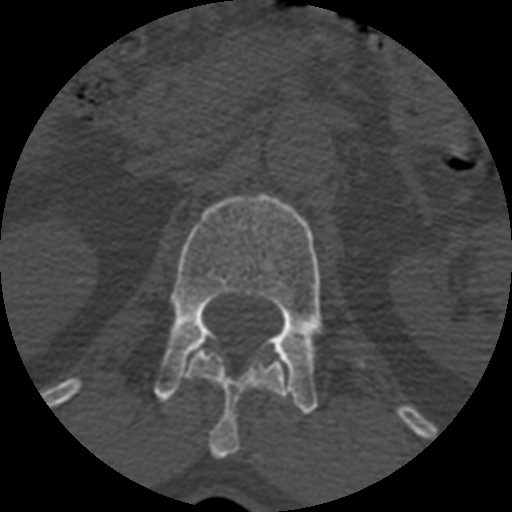
CT including the spine, one axial slice; position 368 of 399 along the scan axis; 120 kVp; bone window (W 1800 / L 400 HU); 1.25 mm slice thickness; 512 × 512 image matrix. Patient age 71 years. Case-level facts recorded for this patient, not image findings: primary cancer: prostate.
Structures marked on this image (semi-automatic segmentation, software-assisted and operator-edited):
- L1 vertebra: bounding box (x1, y1, x2, y2) in pixels: (155, 194, 367, 413)
- T12 vertebra: (185, 348, 289, 459)